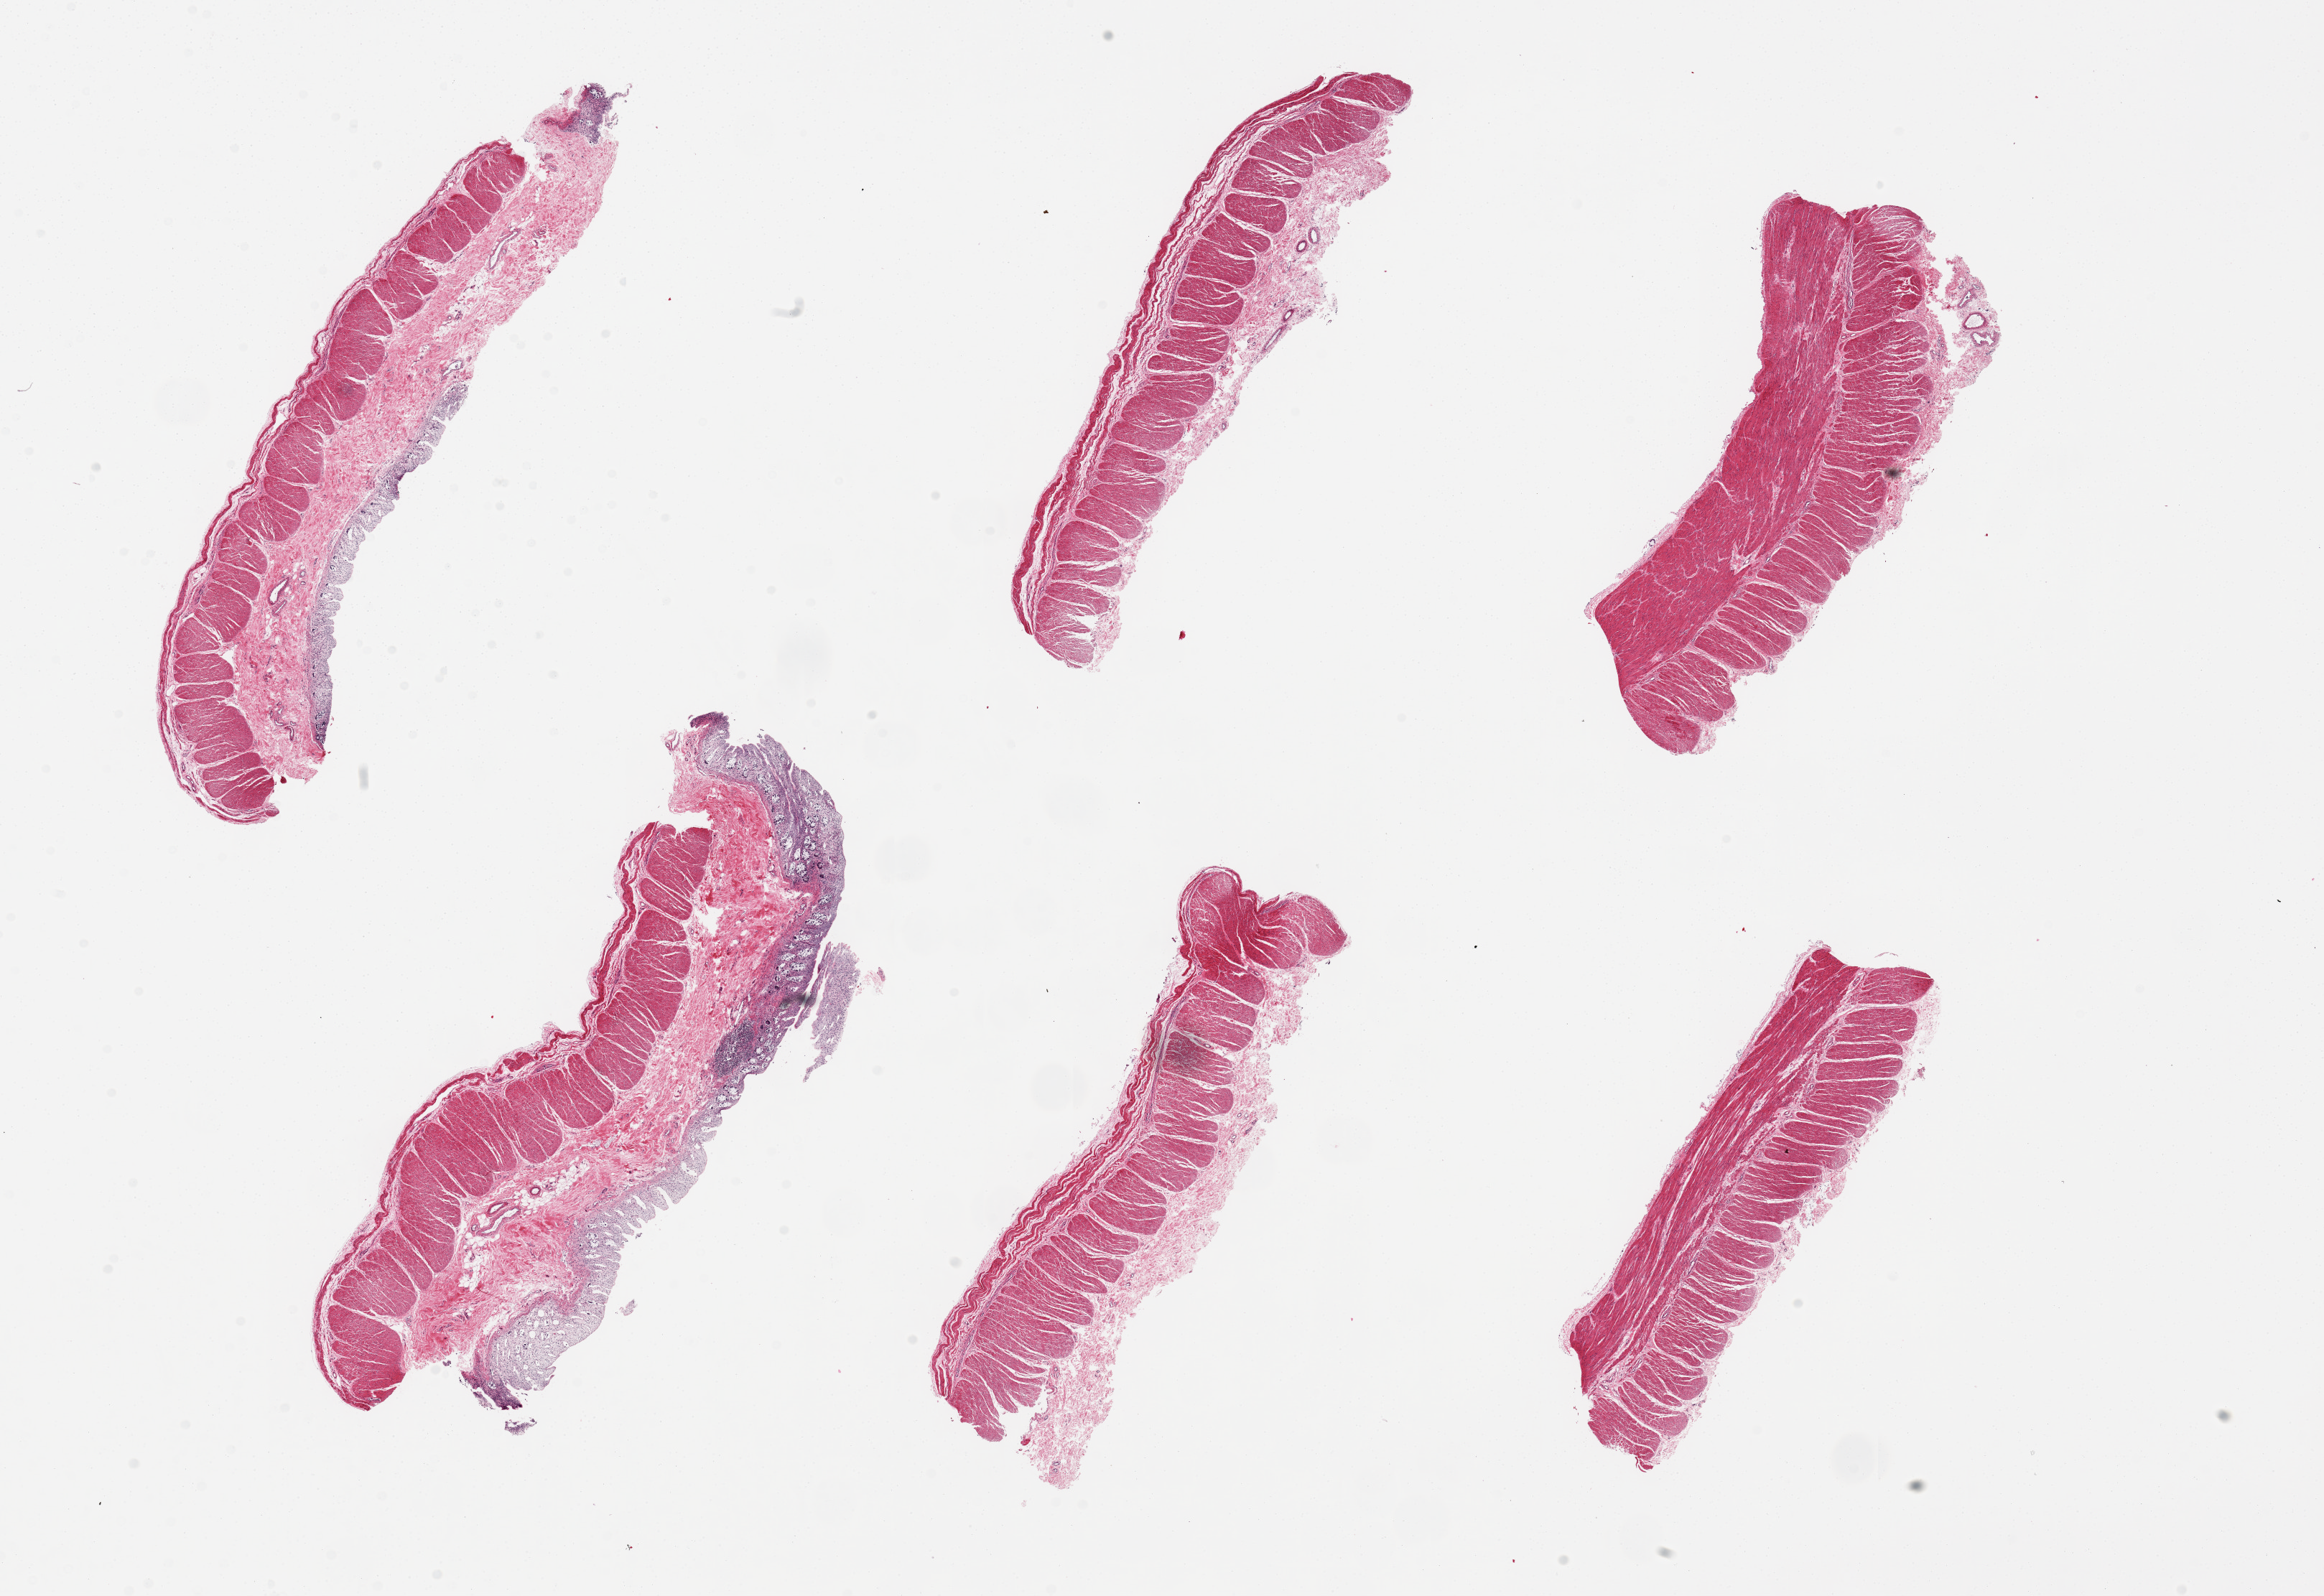
Whole-slide image, haematoxylin and eosin stain, low-resolution overview of the scanned area, about 25.6 x 17.6 mm (from a 20x scan); PAXgene-fixed paraffin-embedded (PFPE) section; sampled site (target tissue): sigmoid colon; donor tissue sample. Male donor.
Review note (as recorded): 6 pieces; all have muscularis; 2 have severely autolyzed colonic mucosa.